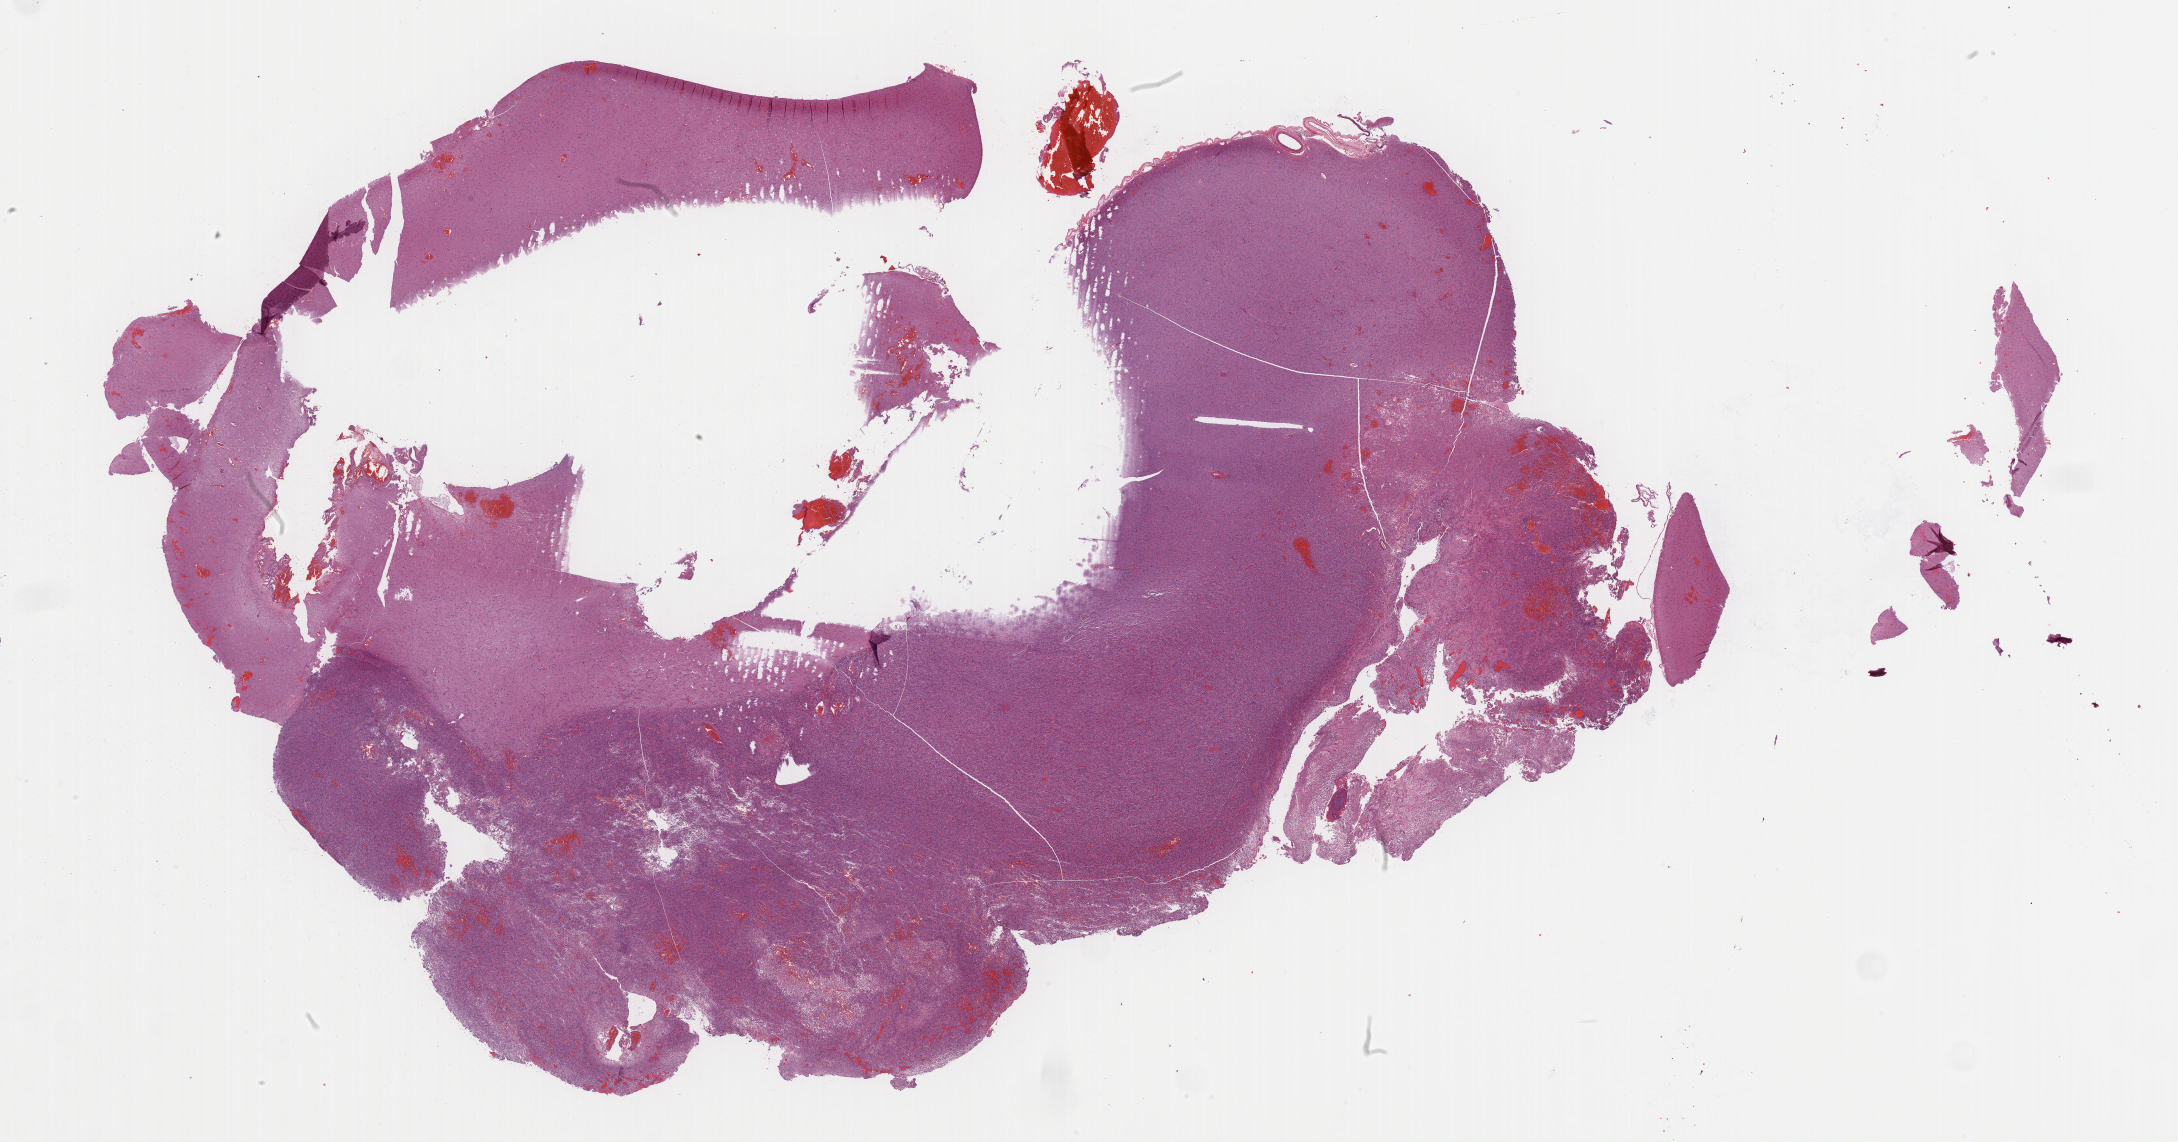
H&E whole-slide image — whole scanned area (about 35.2 x 18.5 mm, from a 40x scan) shown as a low-resolution overview; FFPE section; primary tumour sample from the brain. Male, age 51 years at initial diagnosis.
Pathologic diagnosis: Glioblastoma (frontal lobe).